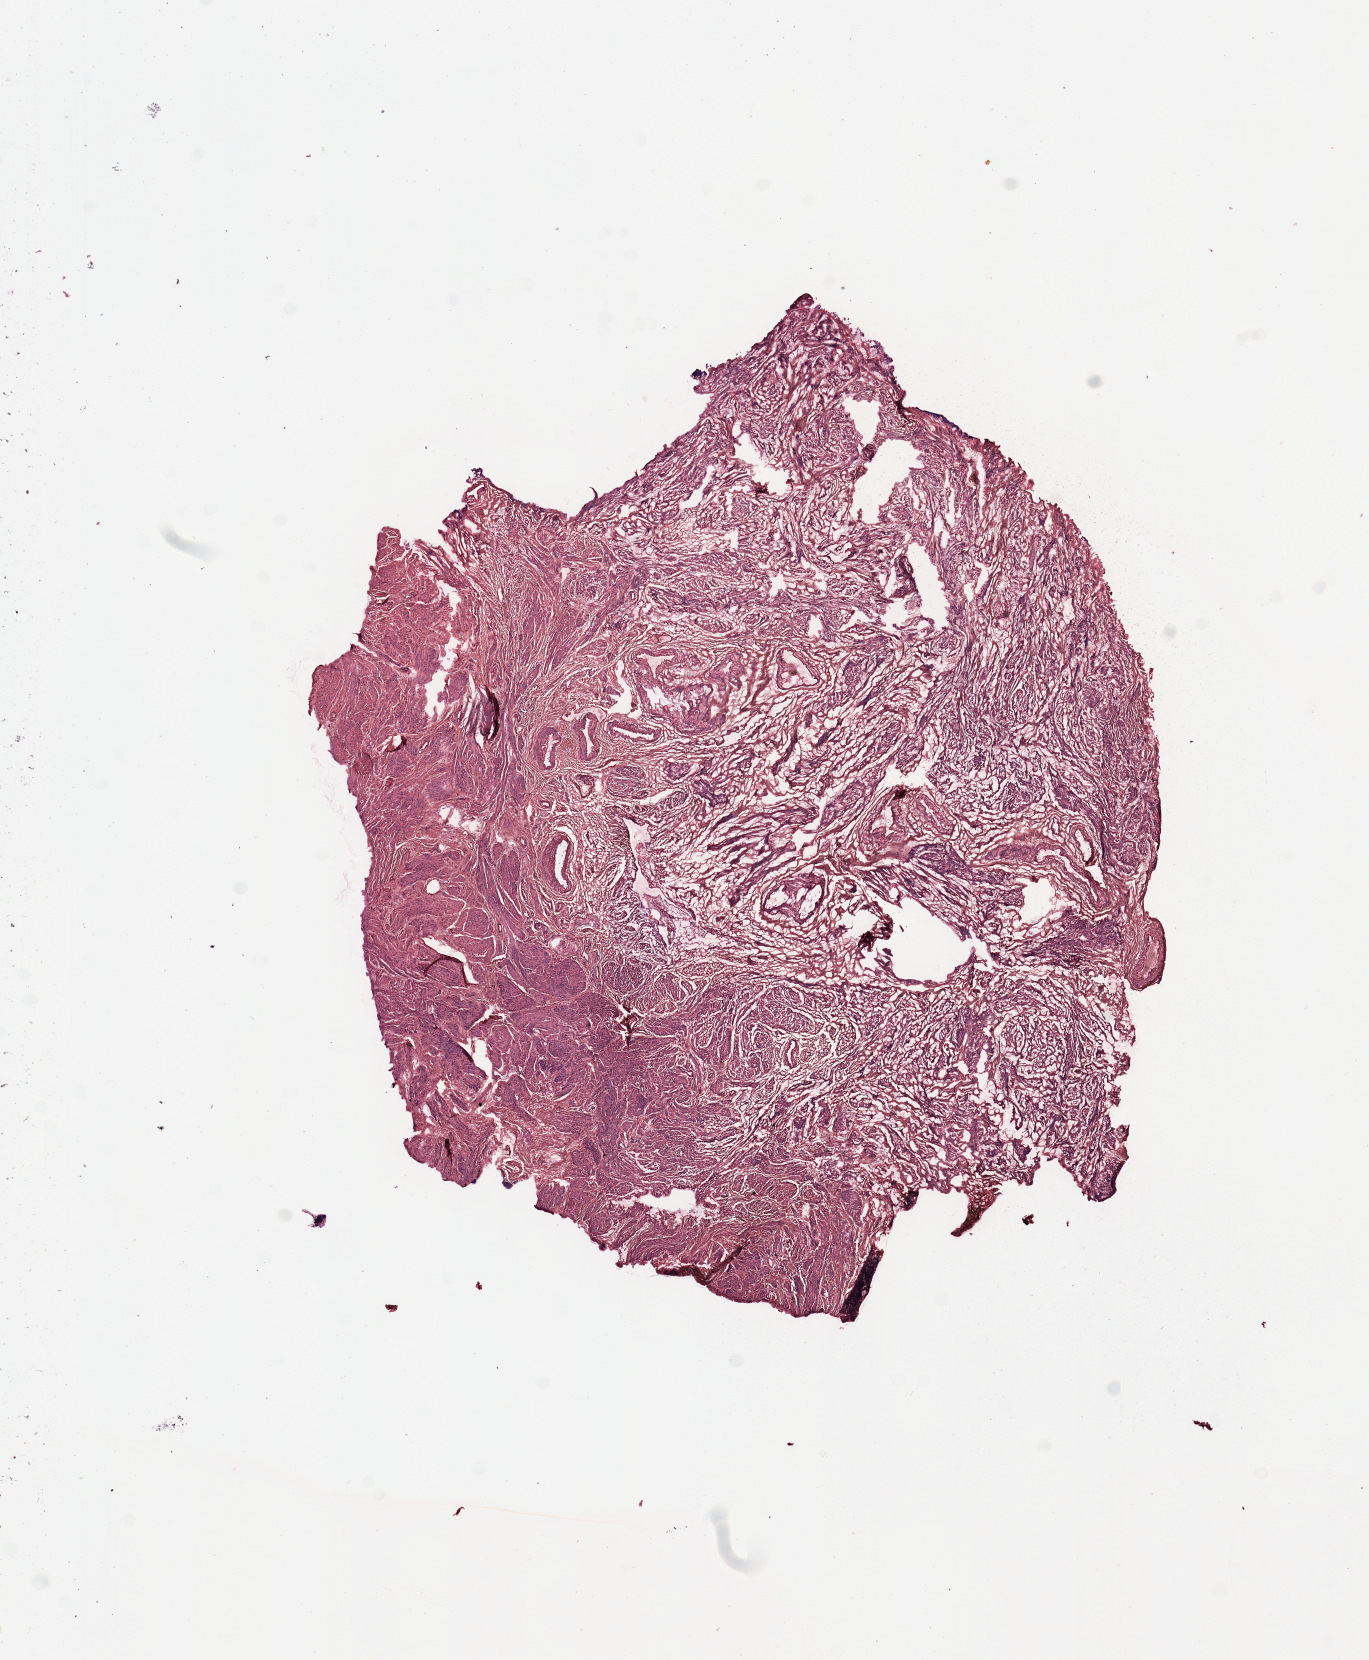
H&E whole-slide image, whole scanned area (about 10.8 x 13.1 mm) shown as a low-resolution overview. Normal (non-tumour) tissue sample, uterus. Female, 65 y/o.
* this section: normal (non-tumour) tissue from the same patient
* patient diagnosis: Endometrioid adenocarcinoma, NOS